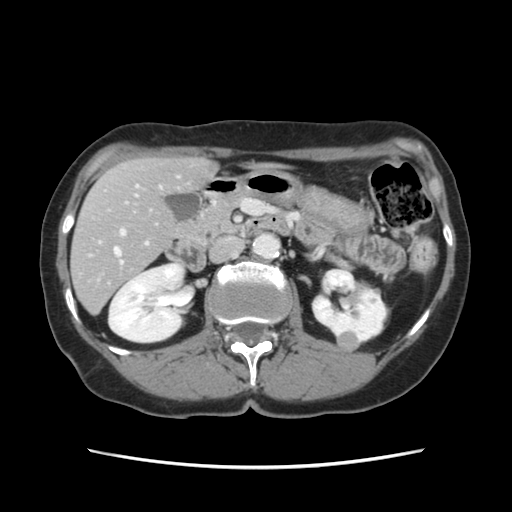
Contrast-enhanced abdominal CT, one axial slice; slice 54 of 120 in the series (ordered by position); 120 kVp; intravenous contrast given; soft-tissue window (W 400 / L 40 HU); 512 × 512 image matrix, field of view 330 × 330 mm. Female patient, age 70 years. Case-level facts recorded for this patient, not image findings: diagnosis: colorectal cancer liver metastases, imaged before liver resection; multiple liver metastases: no; largest metastasis: 2.5 cm; chemotherapy before resection: yes.
Structures marked on this image (expert manual segmentation):
- hepatic veins: box from (x=114, y=248) to (x=122, y=263) px
- liver: (x=72, y=159)–(x=215, y=312)
- planned liver remnant (the part of the liver to remain after resection): (x=72, y=158)–(x=216, y=309)
- portal vein (with intrahepatic branches): (x=99, y=176)–(x=179, y=245)